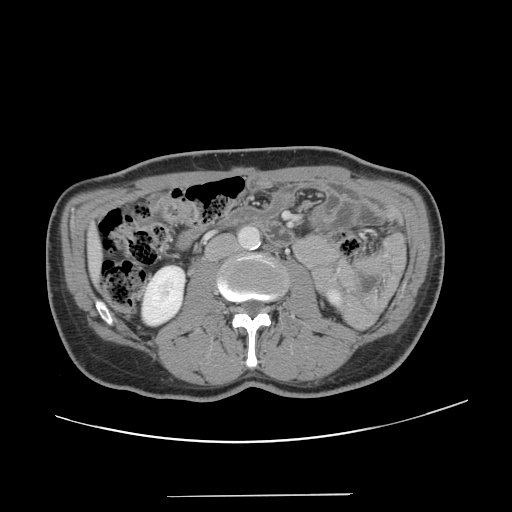
Contrast-enhanced abdominal CT, one axial slice. Position 39 of 131 along the scan axis. Intravenous contrast given. Soft-tissue window (W 400 / L 40 HU). 2.5 mm slice thickness. 512 × 512 image matrix, field of view 403 × 403 mm. Male patient, age 60 years. Case-level facts recorded for this patient, not image findings: diagnosis: colorectal cancer liver metastases, imaged before liver resection; multiple liver metastases: no; largest metastasis: 2.5 cm; disease in both lobes: no.
Outlined on this slice (outlined manually by an expert reader):
- liver: bounding box <90,233,99,275> (left, top, right, bottom; pixels)
- planned liver remnant (the part of the liver to remain after resection): <90,231,99,274>